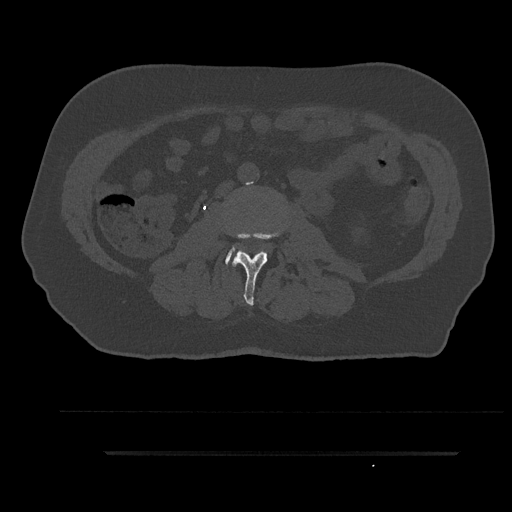
CT including the spine, one axial slice; position 82 of 797 along the scan axis; reconstruction kernel Br40s/3; 120 kVp; bone window (W 1800 / L 400 HU); 0.5 mm slice thickness; 512 × 512 image matrix. Patient: male, 63 years. Case-level facts recorded for this patient, not image findings: primary cancer: renal; vertebrae with lytic lesions (as recorded): T8.
Outlined on this slice (semi-automatically segmented with operator editing):
- L2 vertebra: bounding box [x1, y1, x2, y2] px = [230, 231, 282, 306]
- L3 vertebra: [225, 247, 243, 265]